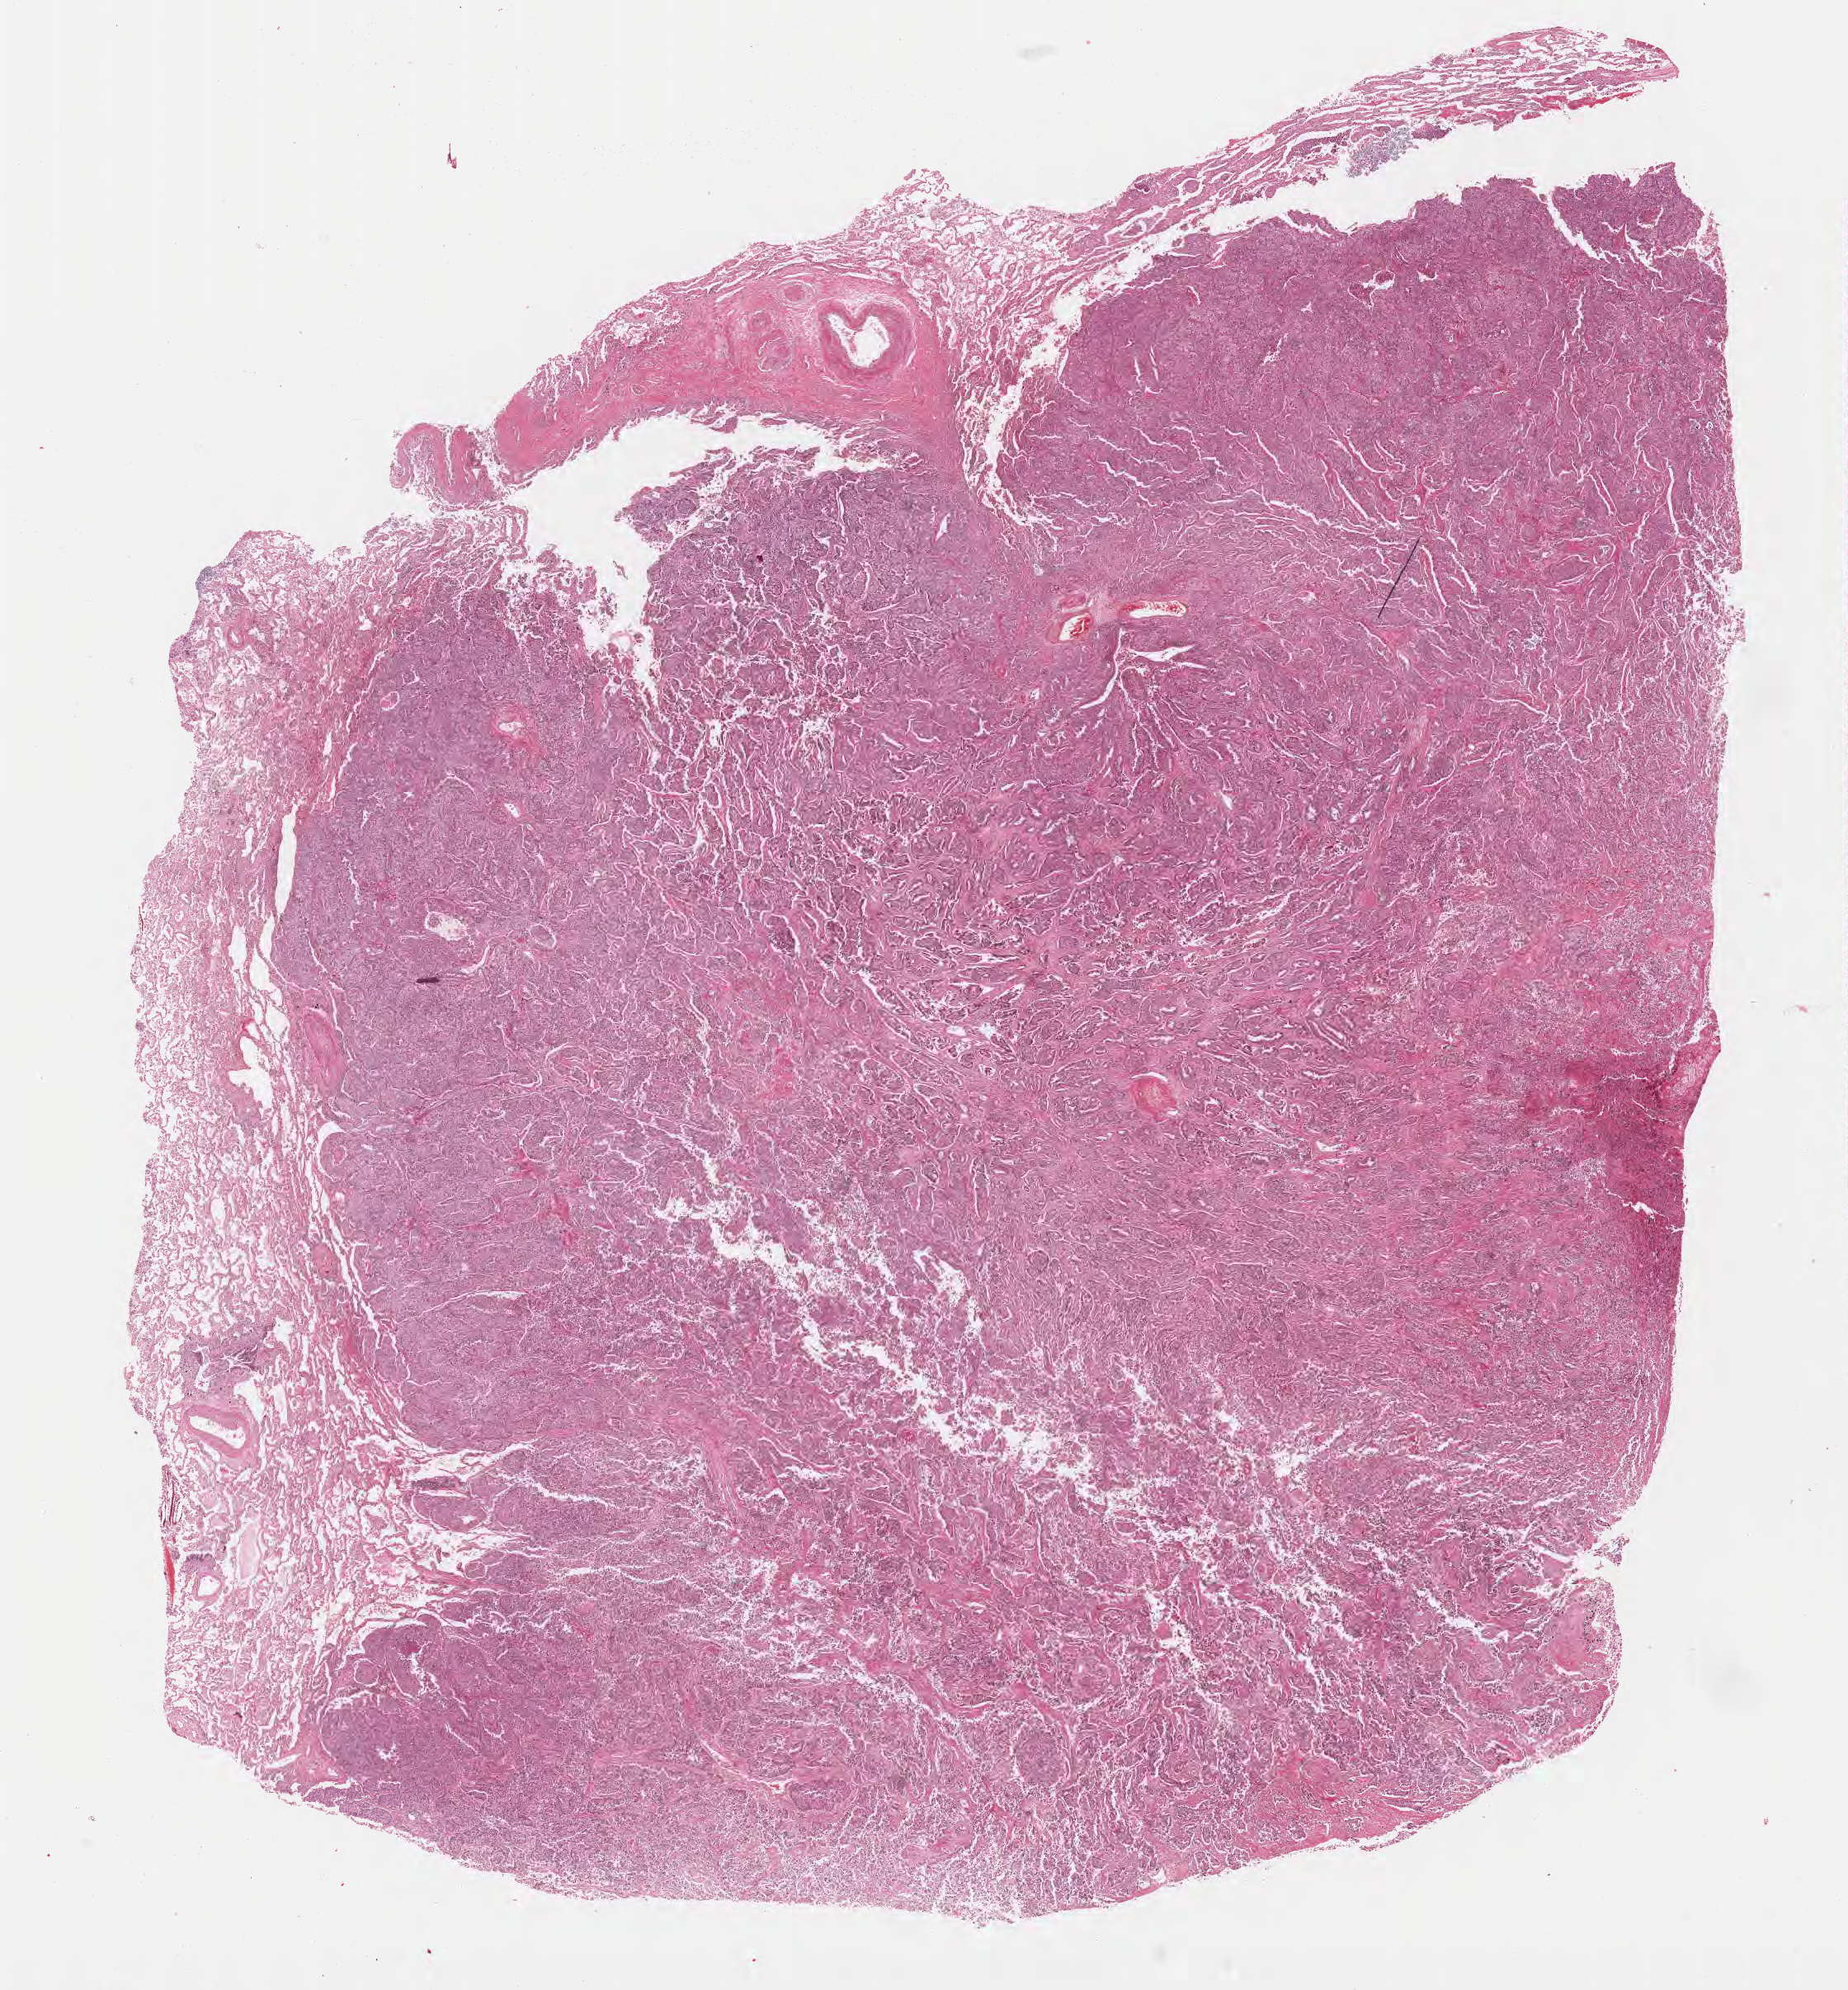
Whole-slide image, haematoxylin and eosin stain — whole scanned area (about 18.1 x 19.5 mm) shown as a low-resolution overview. Formalin-fixed paraffin-embedded section. Specimen: primary tumor. Site: upper lobe of right lung. Patient male; aged 76. Composition of this section per pathologist review: tumor cells 80%, tumor nuclei 80%, stromal cells 15%, necrosis 3%, normal cells 2%. Inflammatory infiltration, as recorded: lymphocyte infiltration 2%, monocyte infiltration 2%, neutrophil infiltration 3%.
AJCC pathologic stage: Stage IIA. Diagnosis: Acinar cell carcinoma. Section: top of the tissue portion.